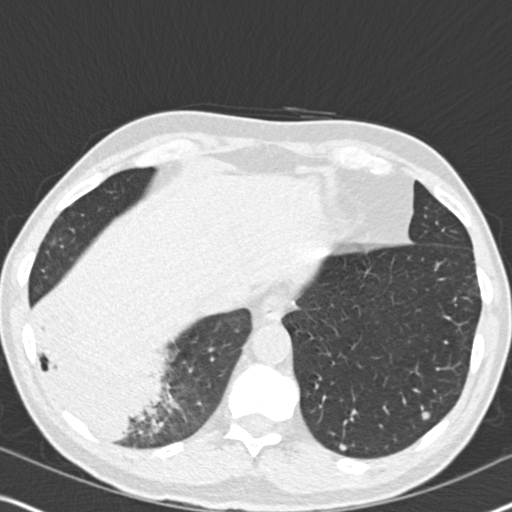
Axial slice from a low-dose chest CT screening exam; second screening round (one year after baseline); lung window (W 1500 / L -600 HU); standard (soft-tissue) reconstruction kernel (B30f). Male, age 61 years at enrolment. Current smoker at enrolment.
Expert-annotated lung lesion, bounding box [x1, y1, x2, y2] px = [21, 282, 181, 455]. Screening reader's record for this exam (one nodule recorded; not confirmed to be the boxed lesion): non-calcified nodule or mass ≥4 mm, right lower lobe, 90 × 80 mm, soft tissue attenuation, pre-existing on the prior screen: yes; interval growth: yes. Official screen result: positive, other. Participant outcome: lung cancer diagnosed 20 days after this screen — bronchiolo-alveolar adenocarcinoma, NOS, right lower lobe, moderately differentiated (G2), stage IIIB (AJCC 6th edition), 90 mm at pathology.